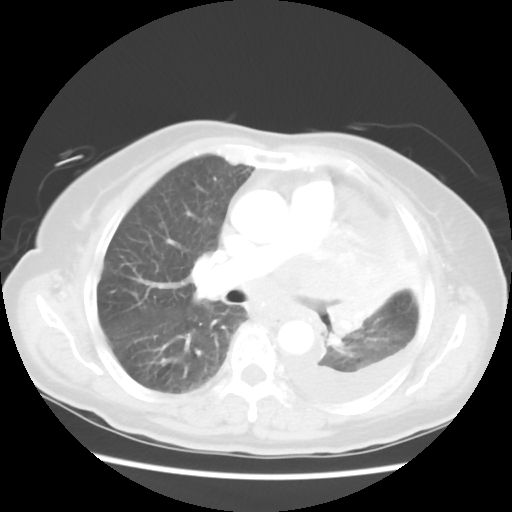
Chest CT, one axial slice; slice 32 of 52 in the series (ordered by position); reconstruction kernel STANDARD; 120 kVp; lung window (W 1500 / L -600 HU); 5 mm slice thickness; 512 × 512 image matrix, field of view 336 × 336 mm. Patient: female, 72 years. Case-level facts recorded for this patient, not image findings: clinical TNM (as recorded): T4 N3 M1b; histopathological grade: G3.
Structures marked on this image (bounding box drawn by a radiologist):
- lung tumour (recorded histology: large cell carcinoma): bounding box (x1, y1, x2, y2) in pixels: (307, 248, 382, 344)